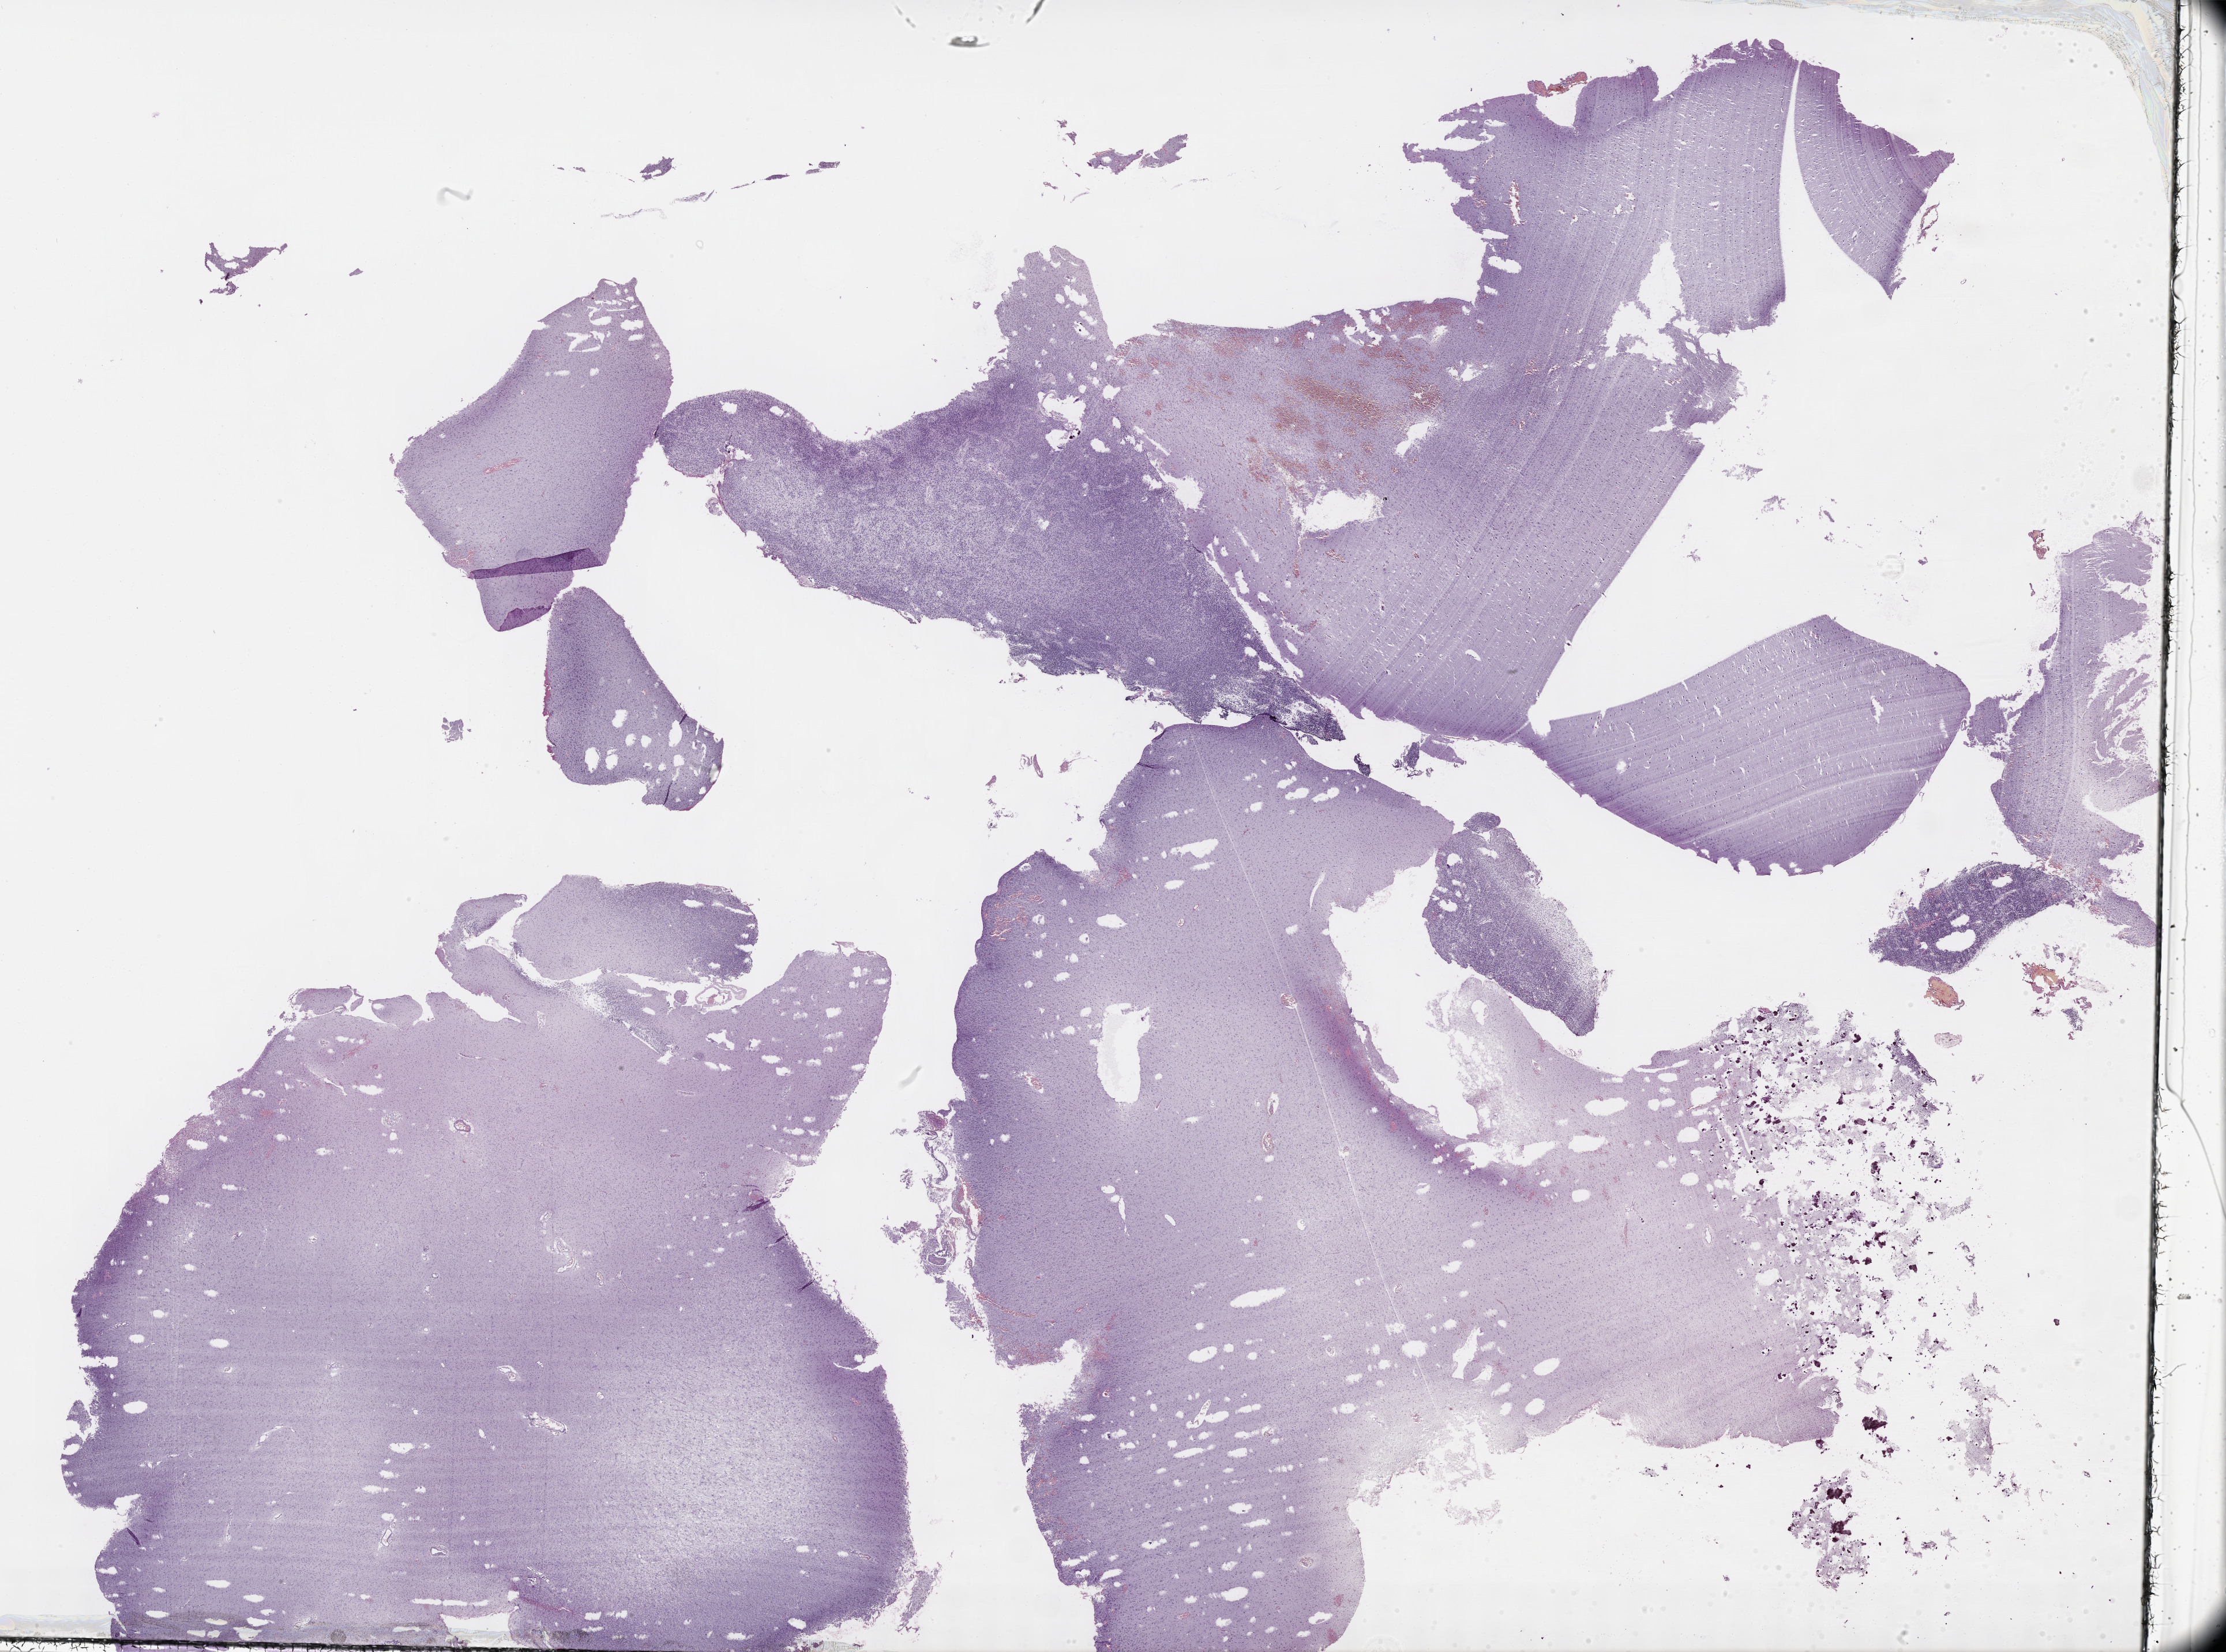
Digitized Hematoxylin and eosin (H&E) stained tissue section (whole slide) — low-resolution overview of the scanned area, about 31.2 x 23.2 mm (acquisition: 40x scan); FFPE section; sample: primary tumour, brain. Patient: female, age at initial diagnosis 34 years. Histologic grade: G3 (poorly differentiated).
• histologic diagnosis: Astrocytoma, anaplastic (cerebrum)
• laterality: right